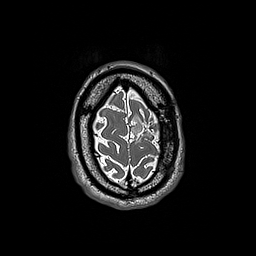
Brain MRI from a brain-tumour surgery series, one axial slice; position 38 of 192 along the scan axis; 1 mm slice thickness; 256 × 256 image matrix, field of view 250 × 250 mm. Case-level facts recorded for this patient, not image findings: histopathology: Oligodendroglioma; WHO grade: 3; IDH mutation: yes.
Outlined on this slice (manually delineated by an expert):
- tumour: bounding box <131,115,146,142> (left, top, right, bottom; pixels)